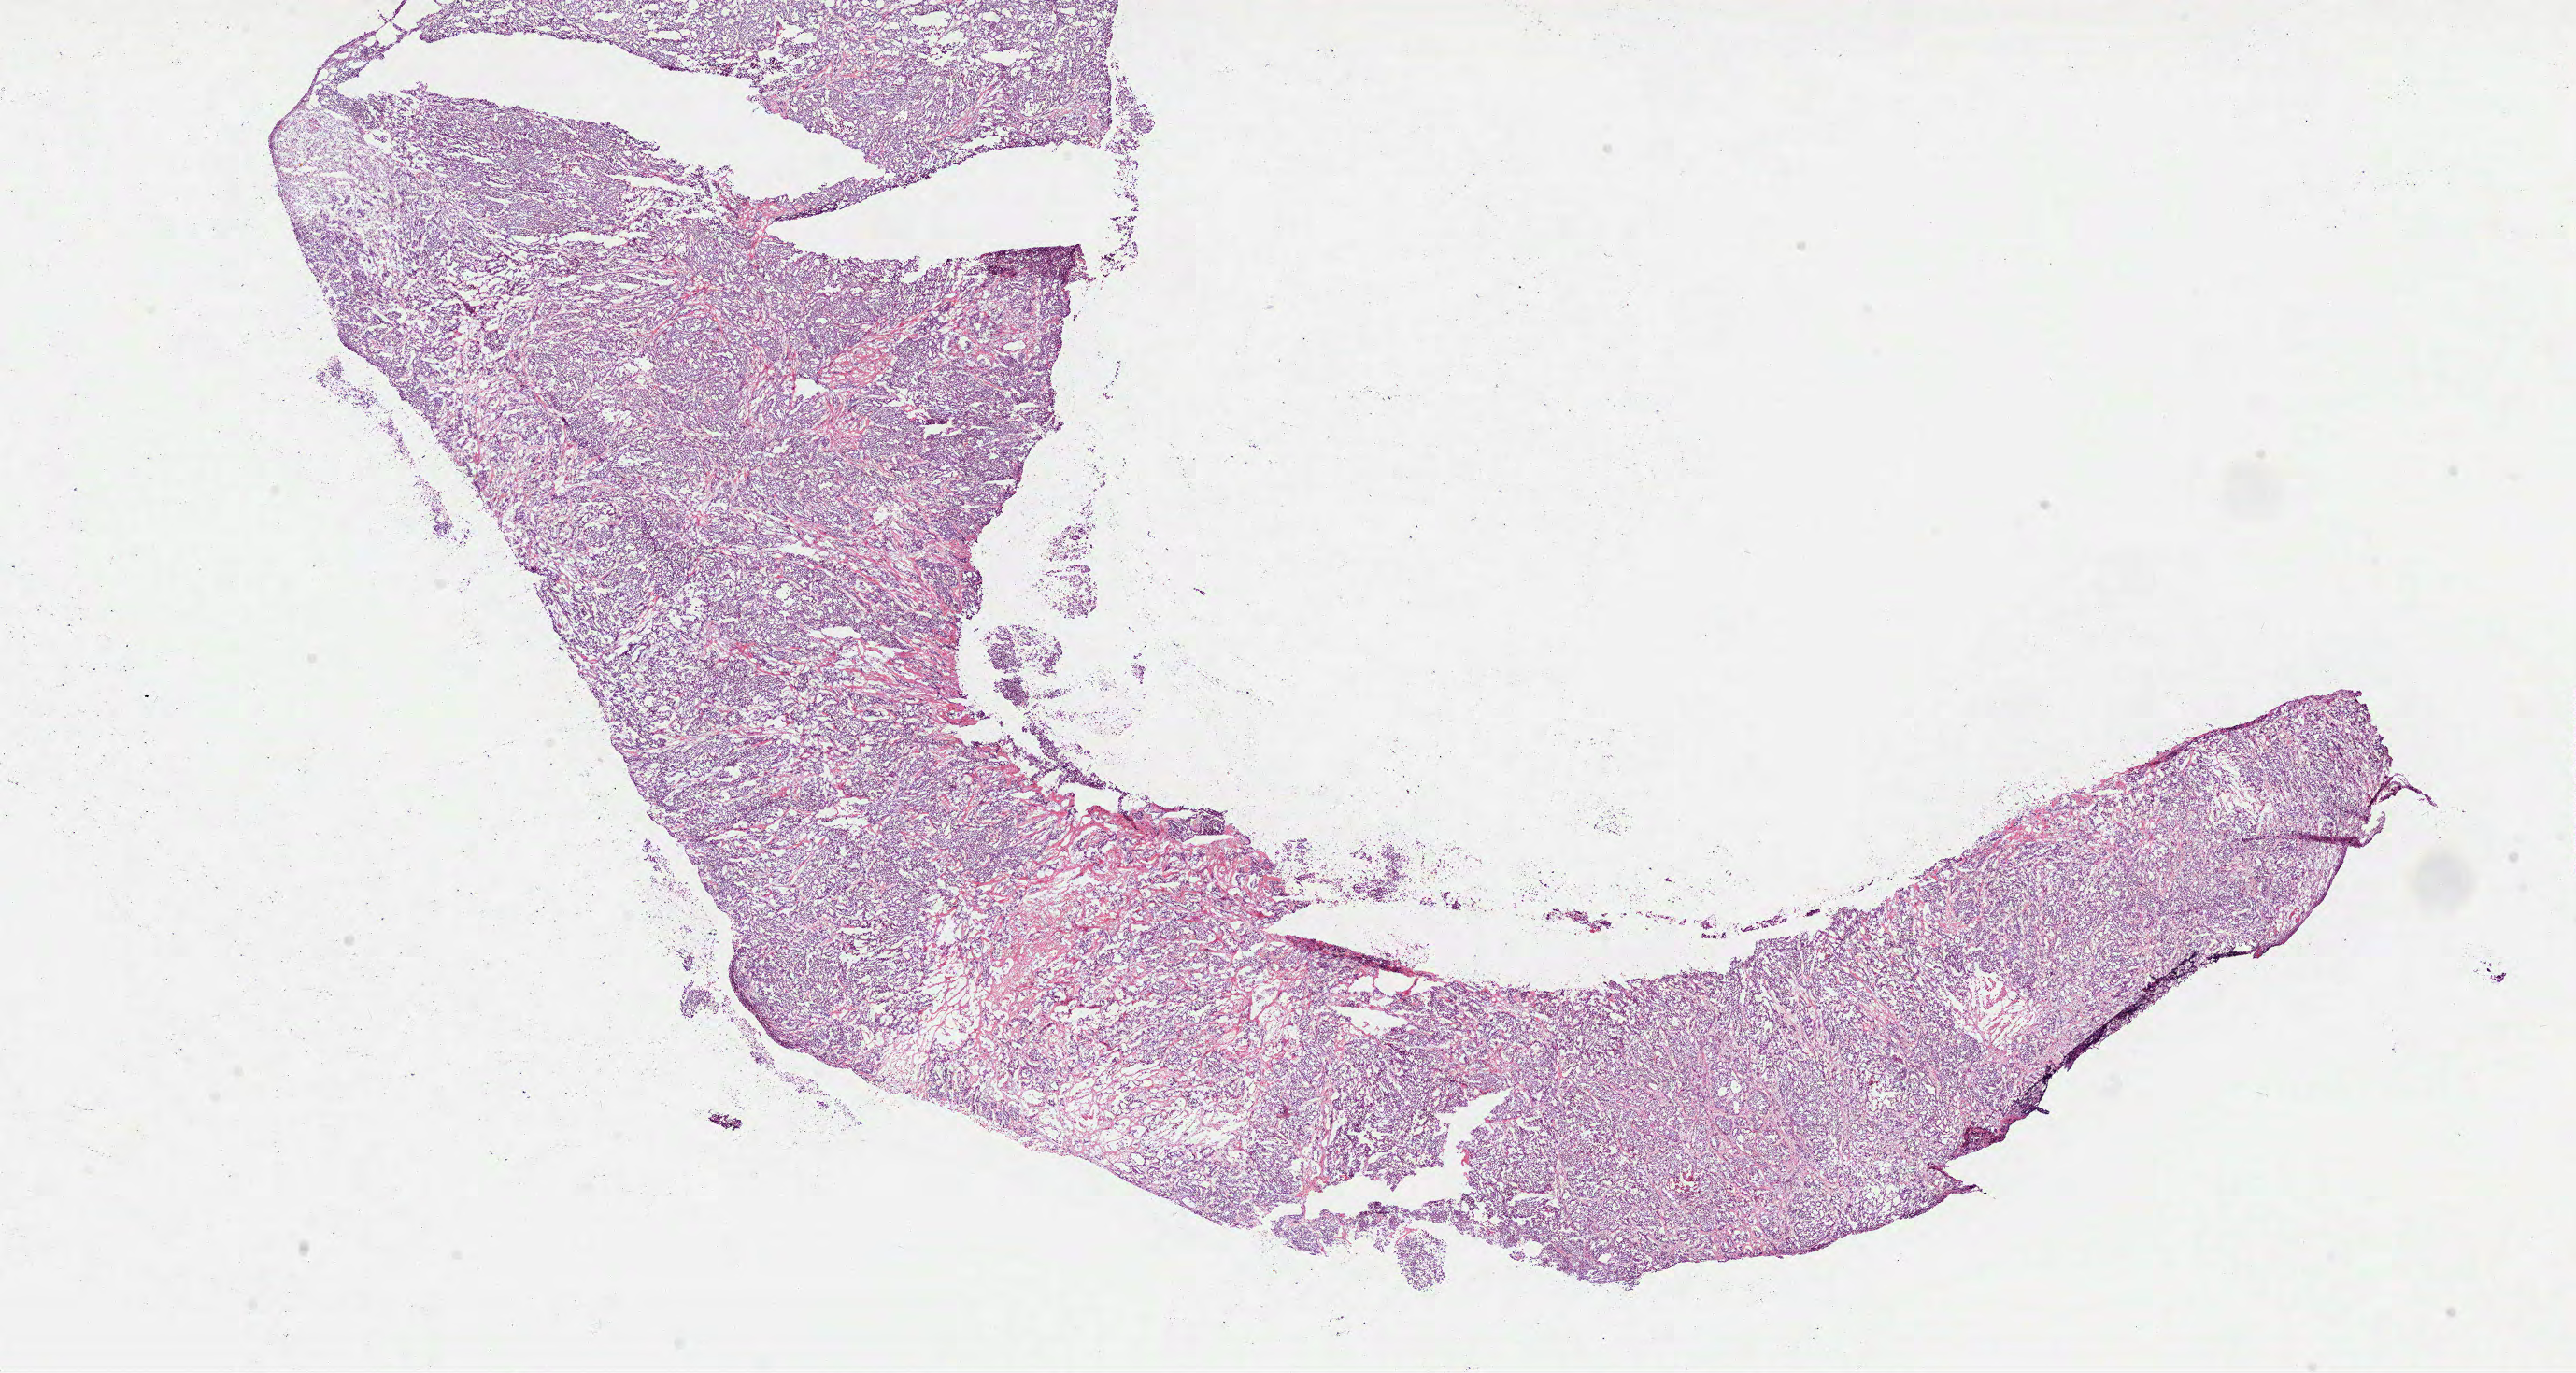
Digitized H&E-stained tissue section (whole slide), low-resolution overview of the scanned area, about 22.2 x 11.8 mm, frozen section from the top of the tissue portion, recurrent tumour sample from the lung. Patient: male, age at initial diagnosis 62 years. Slide review estimates, as recorded: tumour cells 99%, tumour nuclei 85%, normal cells 0%, stromal cells 0%, necrosis 1%. Infiltration values recorded for this section: lymphocyte infiltration 2%, monocyte infiltration 0%, neutrophil infiltration 0%.
- this section: recurrent tumour
- patient diagnosis: Adenocarcinoma with mixed subtypes (upper lobe, lung)